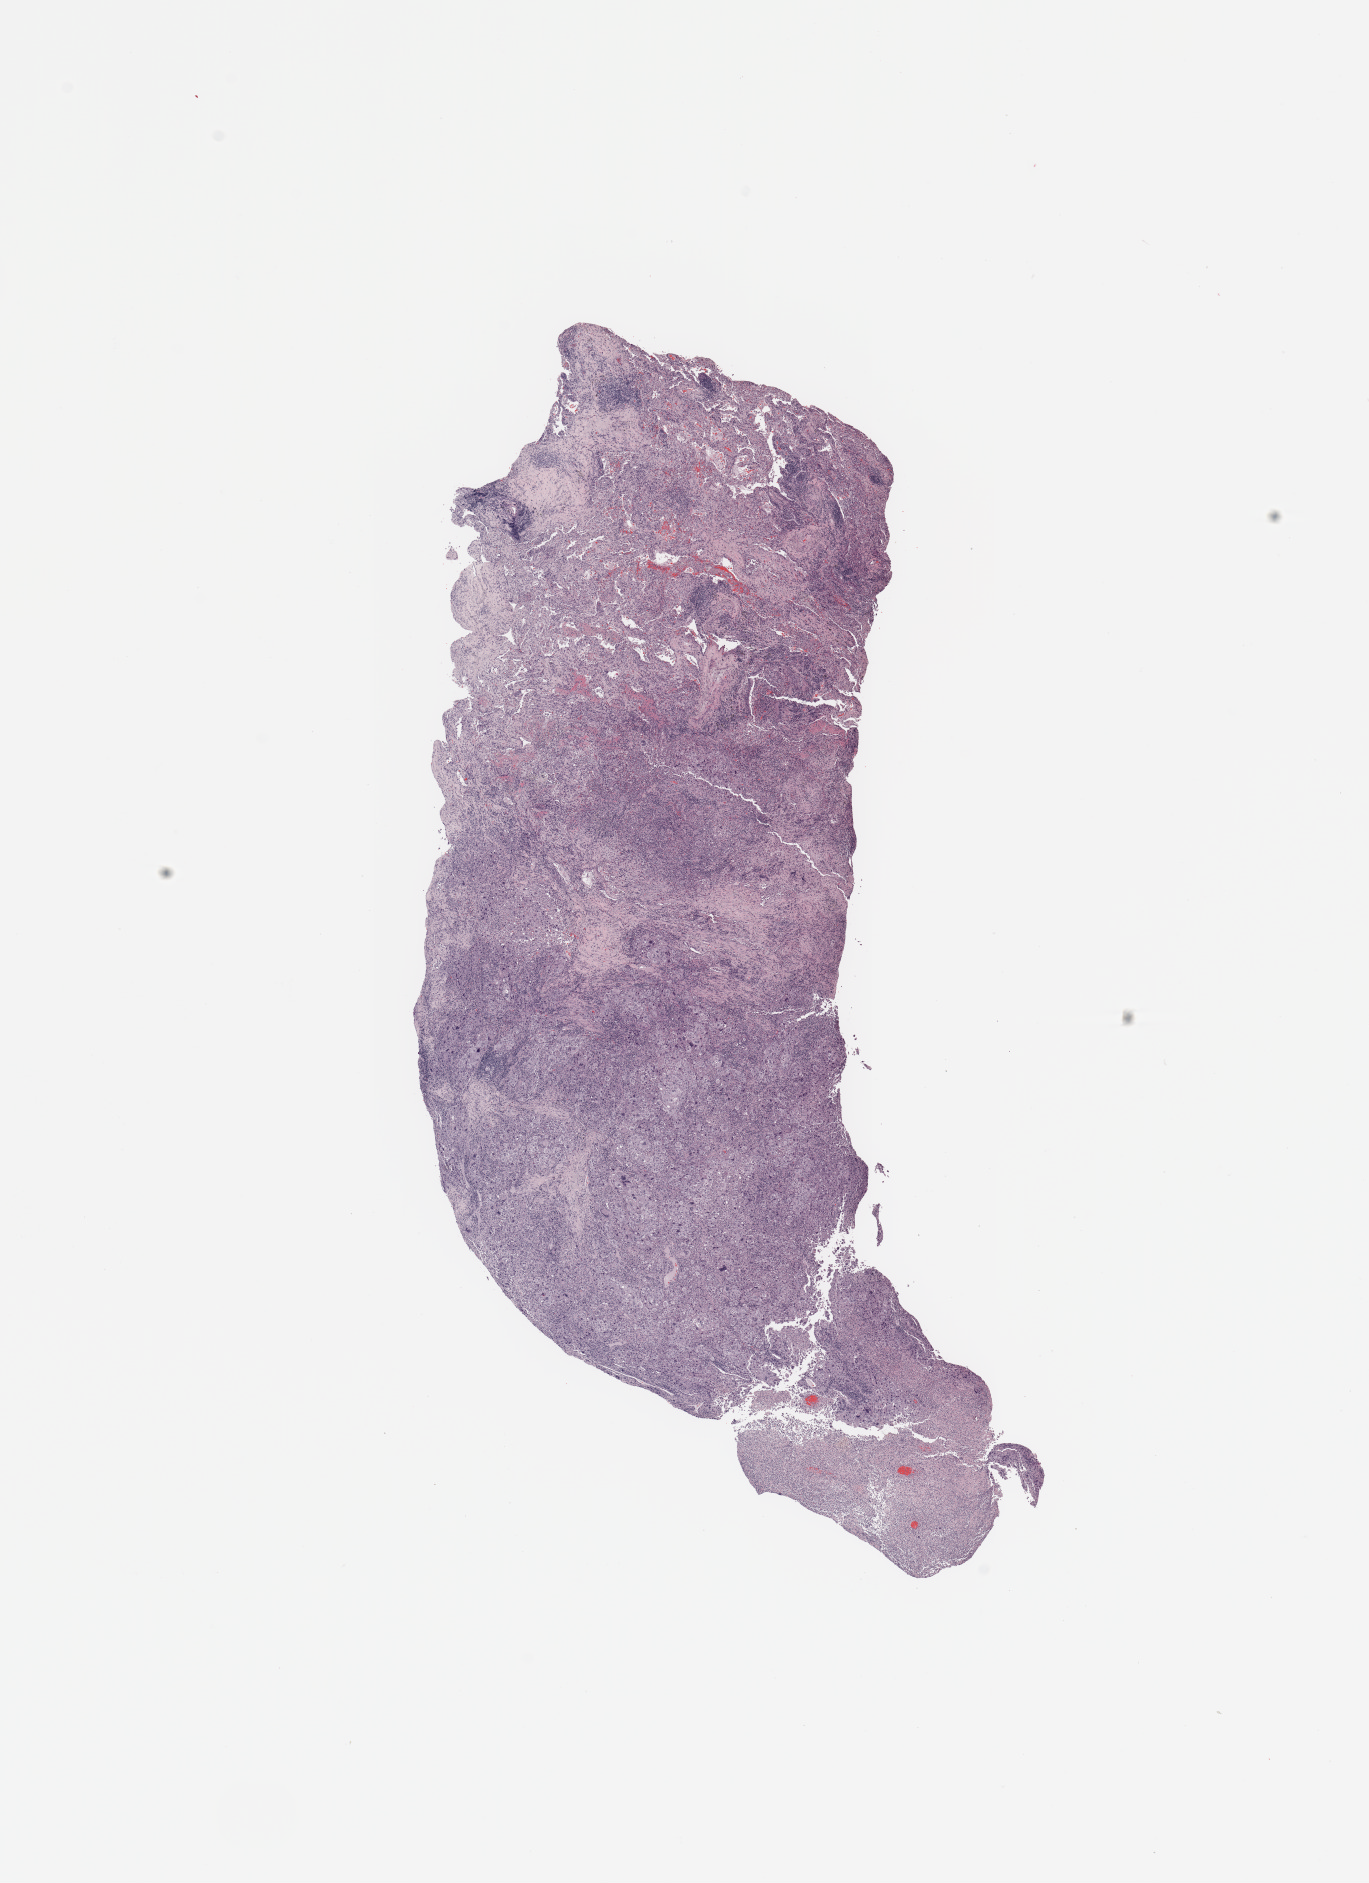
Whole-slide histology image, H&E, a low-resolution overview of the entire scanned area, about 10.8 x 14.9 mm (slide scanned at 20x); lung, tumour tissue. 66-year-old female patient. Histologic grade: G3 (poorly differentiated).
* diagnosis: Adenocarcinoma, NOS
* AJCC pathologic stage: IIA